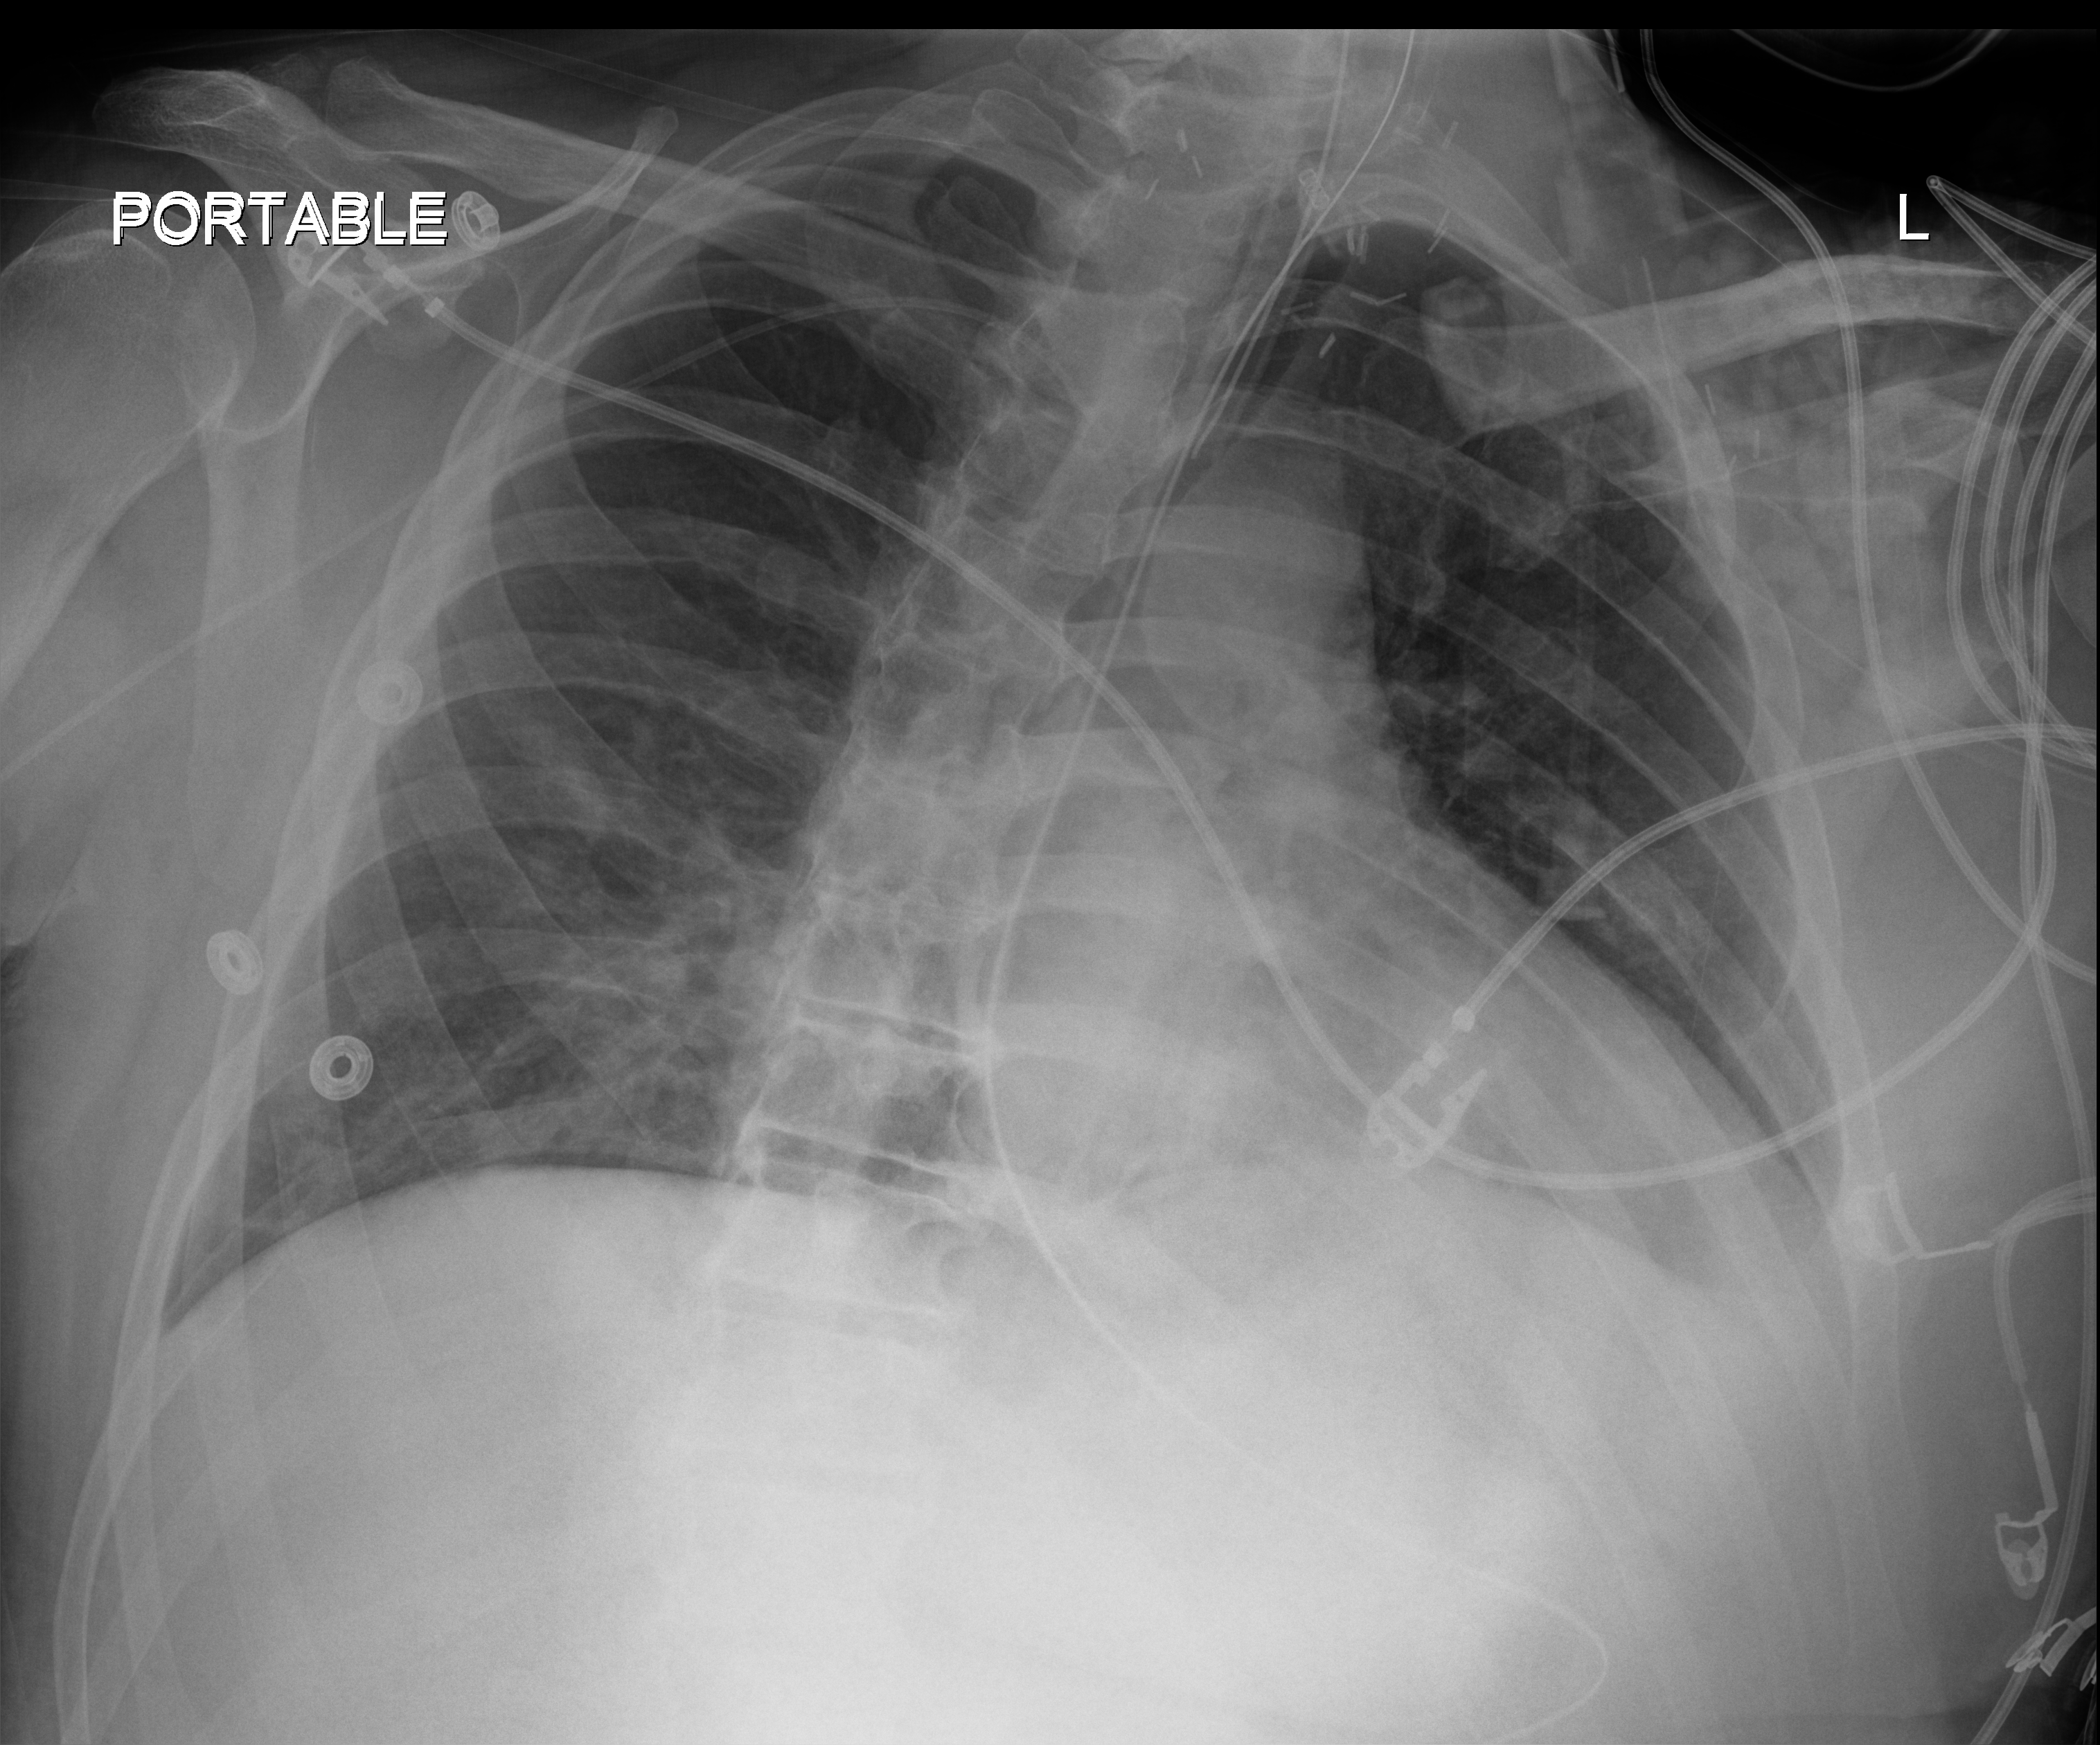
Chest X-ray (portable); anteroposterior (AP) projection. Patient hospitalised with COVID-19, aged 18–59 years.
Hospital-stay facts (about this admission, not read from this image; timing relative to this image not recorded):
- length of hospital stay: 19 days